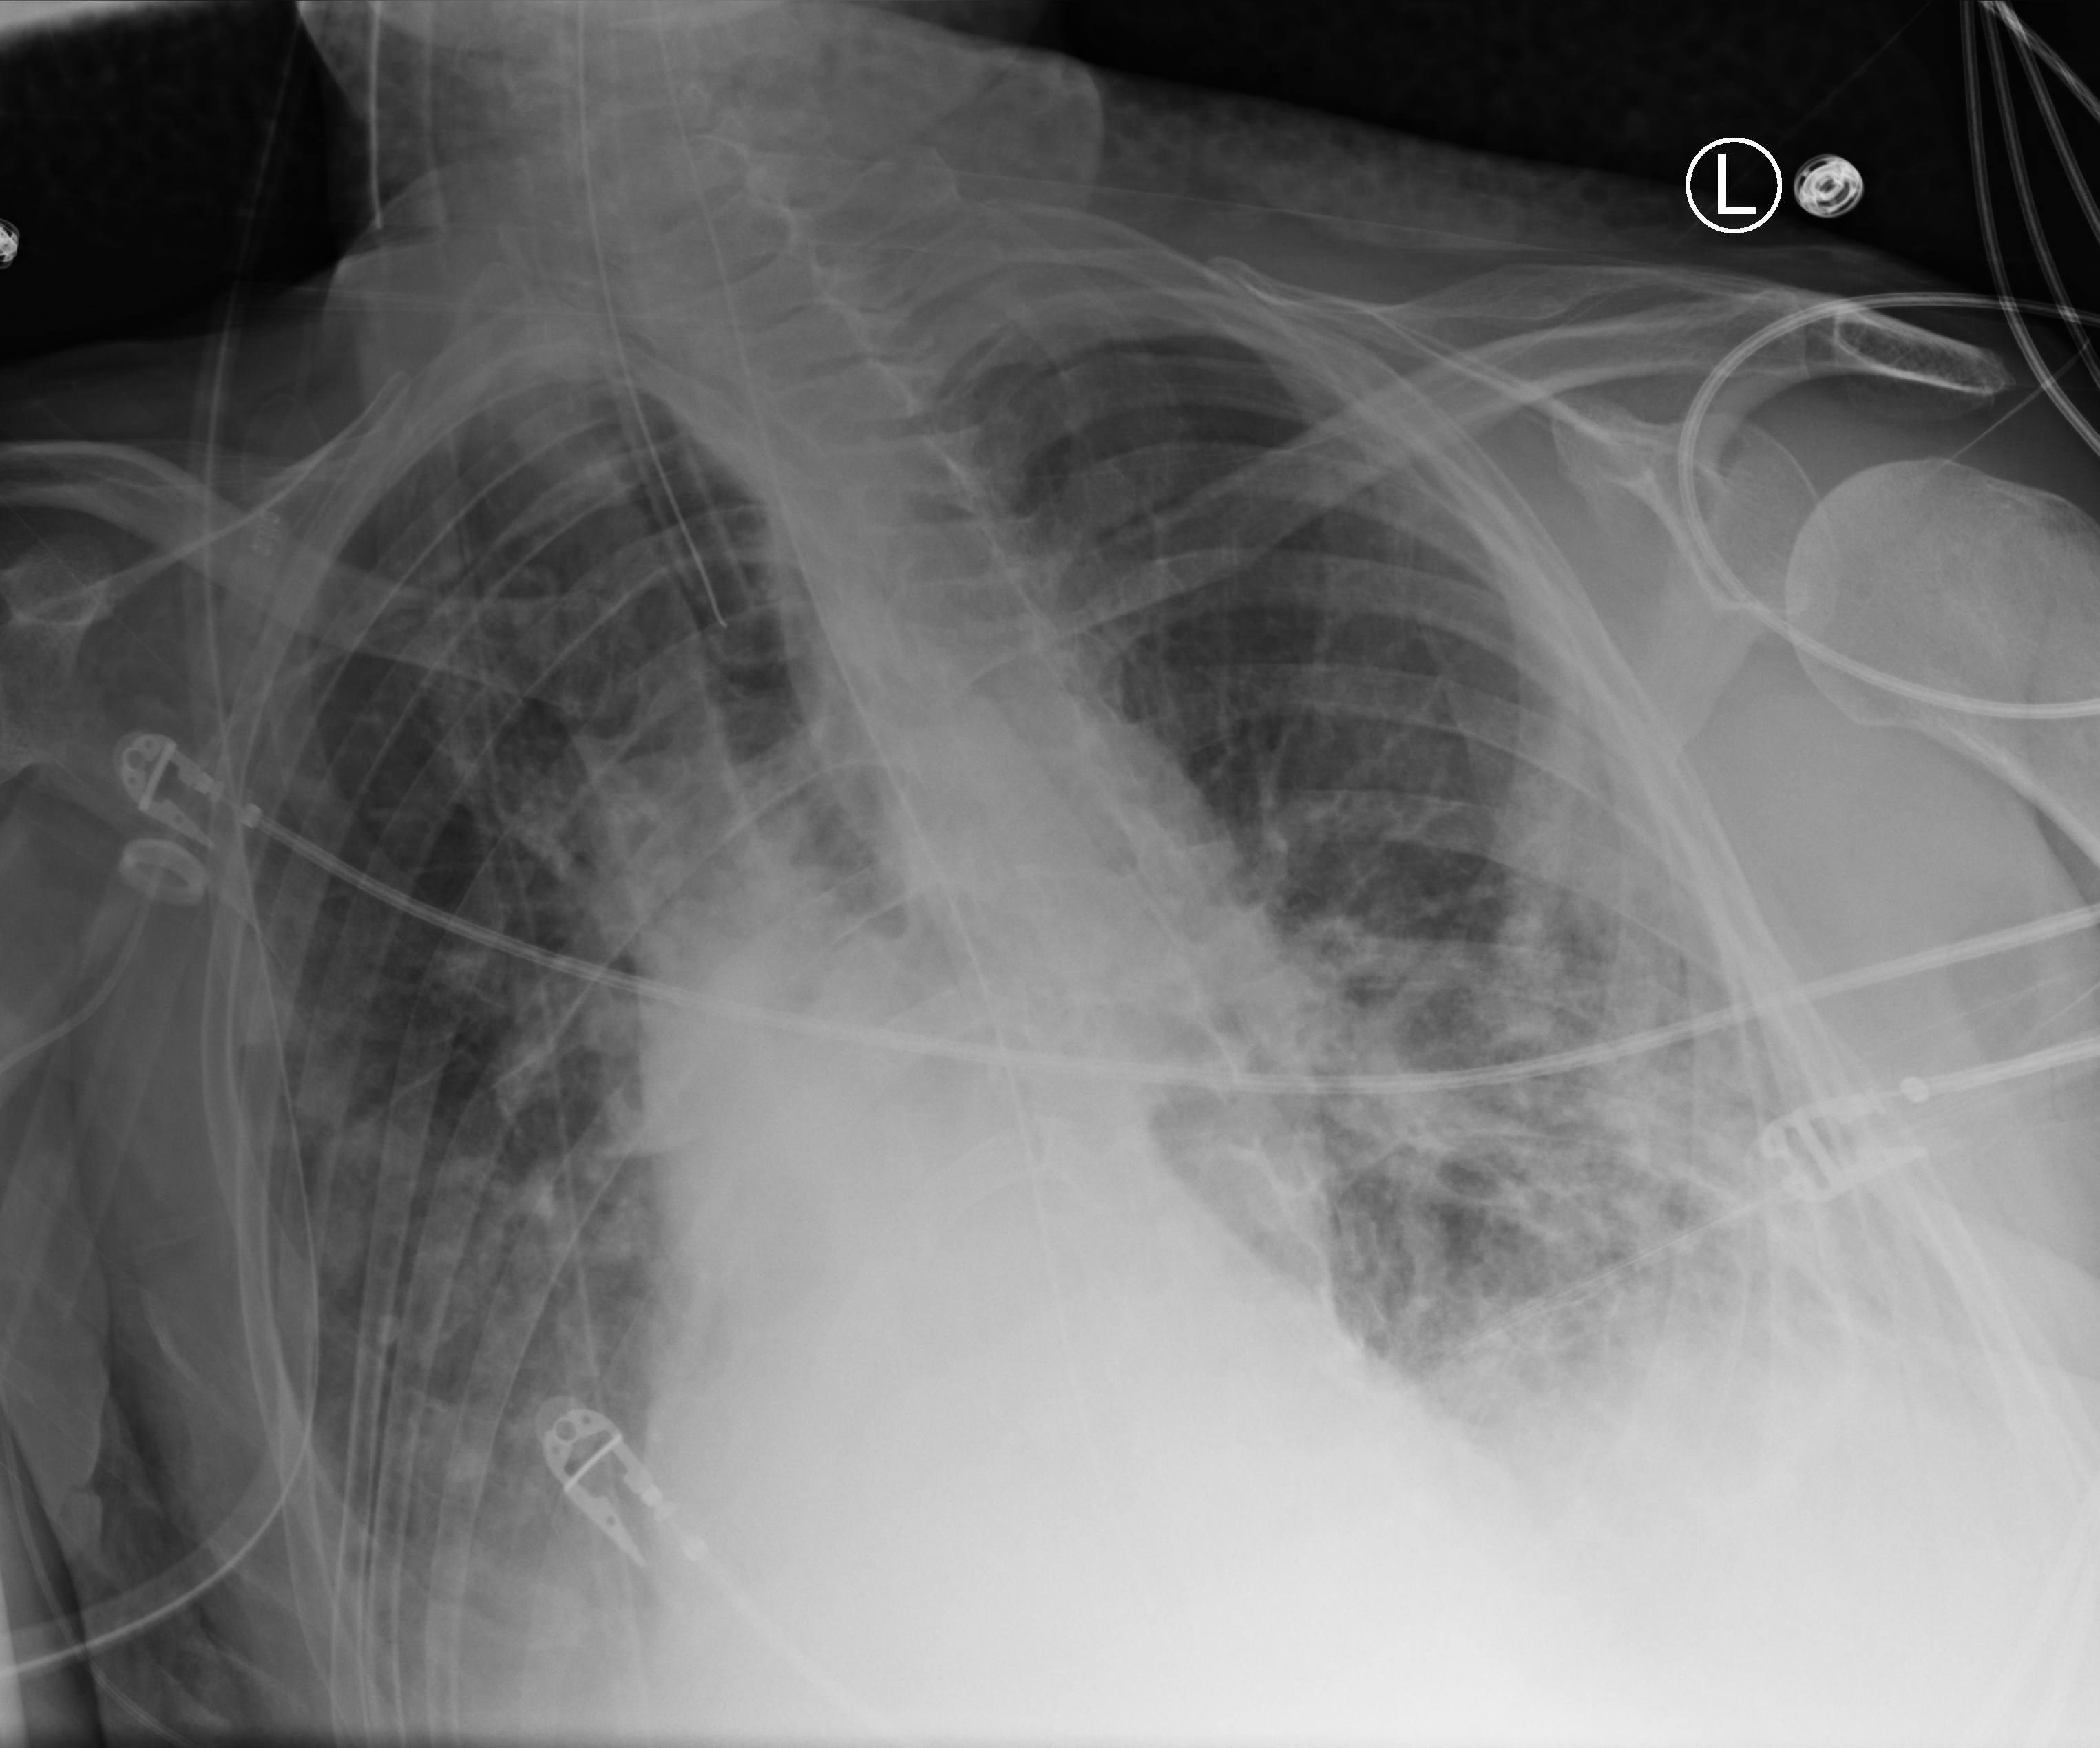
Bedside chest radiograph (computed radiography); anteroposterior (AP) projection. Male patient hospitalised with COVID-19, age 75–90 years.
From the hospital-stay record, not from the radiograph (when in the stay this image was taken is not recorded):
- mechanically ventilated during this hospital stay: yes